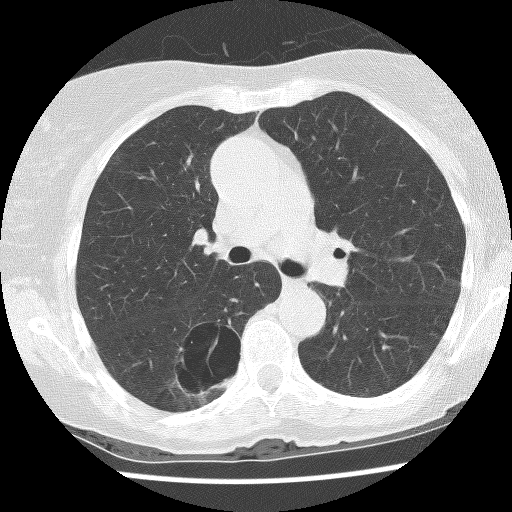
Axial slice from a low-dose chest CT screening exam; baseline annual screen; lung window (W 1500 / L -600 HU); 2.5 mm slice thickness; lung (sharp) reconstruction kernel (BONE); 120 kVp. Female, age 69 years at enrolment. Former smoker at enrolment.
Expert-annotated lung lesion, bounding box (x1, y1, x2, y2) in pixels: (161, 321, 246, 396). The screening reader recorded 2 non-calcified nodules or masses ≥4 mm on this exam (right lower lobe, right lower lobe); which of them this box marks is not recorded. Later outcome: lung cancer diagnosed 288 days after this screen — non-small cell carcinoma, right lower lobe, poorly differentiated (G3), stage IB (AJCC 6th edition), 36 mm at pathology.